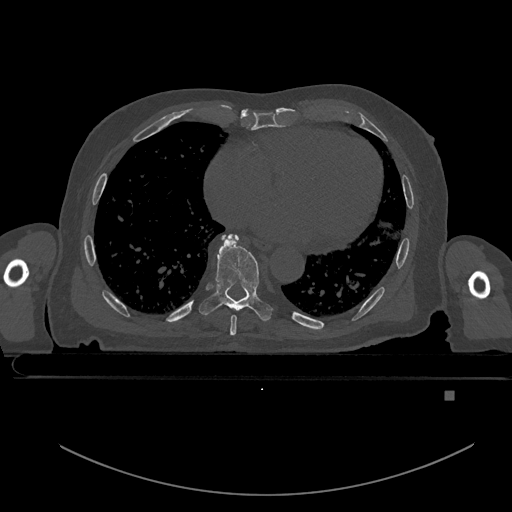
CT including the spine, one axial slice; position 210 of 969 along the scan axis; bone window (W 1800 / L 400 HU); 0.5 mm slice thickness; 512 × 512 image matrix, field of view 456 × 456 mm. Male patient, age 82 years. Case-level facts recorded for this patient, not image findings: primary cancer: prostate.
Structures marked on this image (semi-automatically segmented with operator editing):
- T7 vertebra: bounding box [x1, y1, x2, y2] px = [229, 236, 237, 335]
- T8 vertebra: [199, 235, 273, 321]